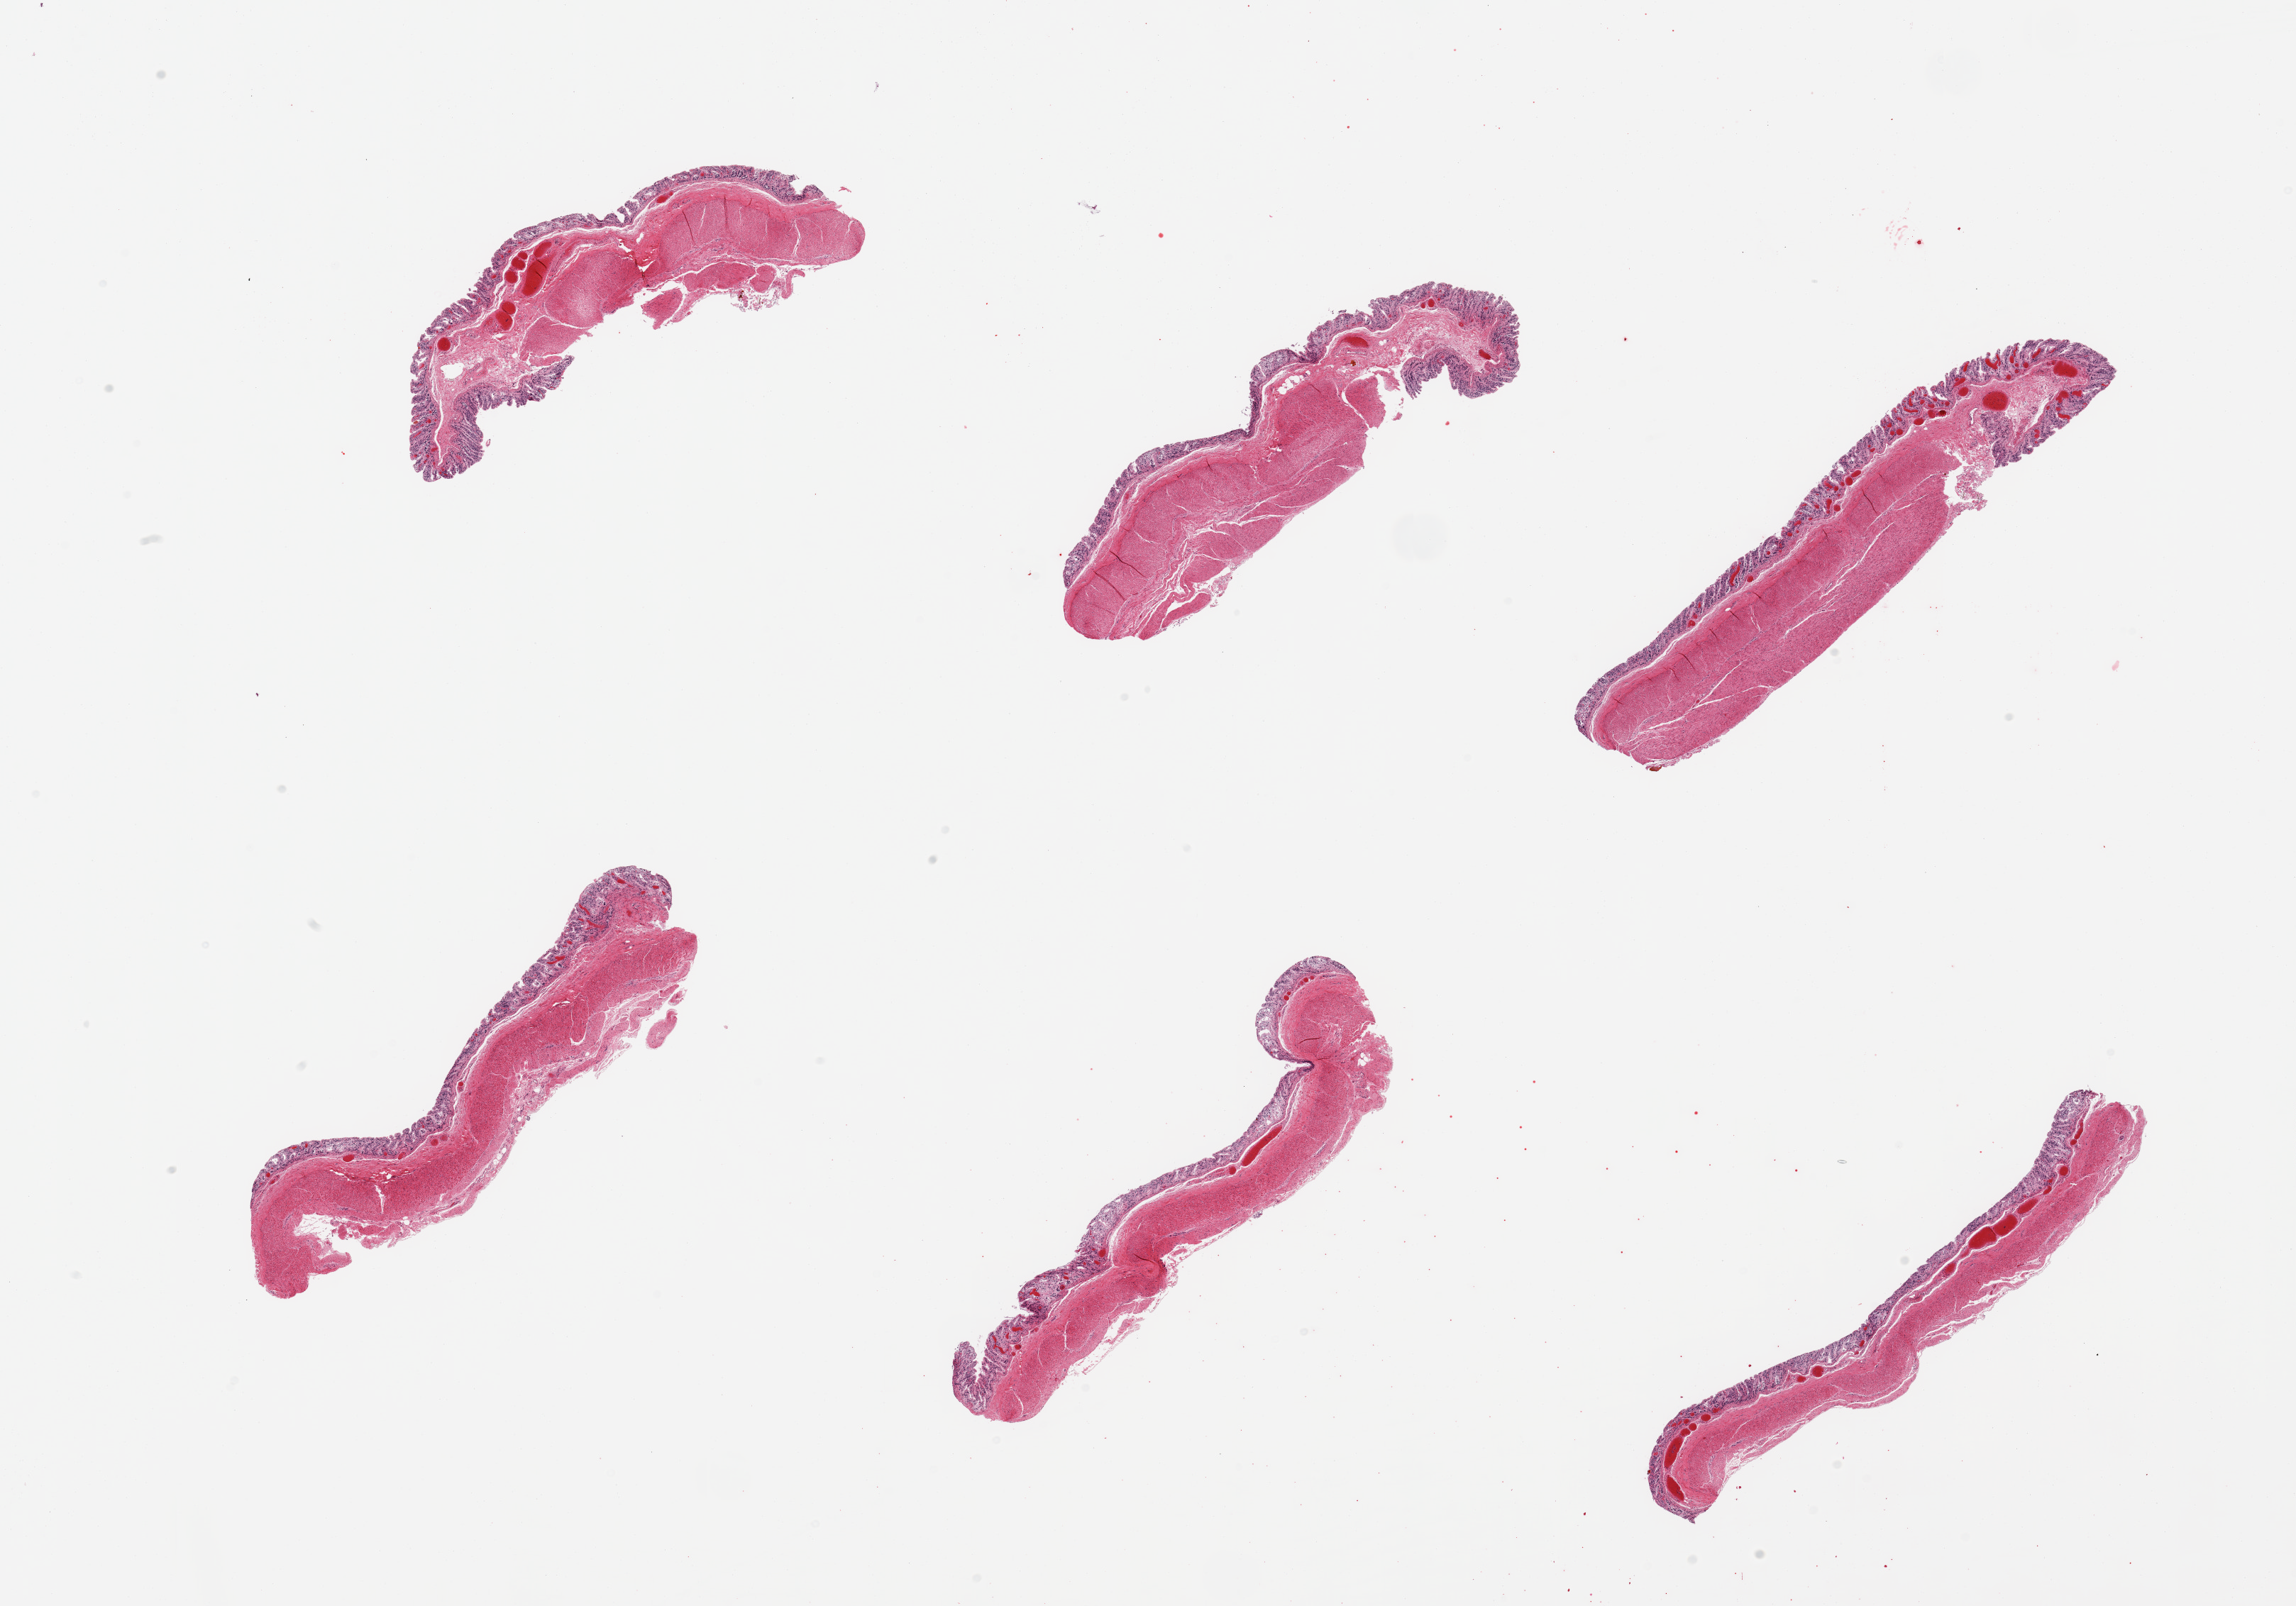
Haematoxylin and eosin whole-slide image, whole scanned area (about 25.6 x 17.9 mm) shown as a low-resolution overview. PAXgene-fixed, paraffin-embedded tissue. Sampled site (target tissue): transverse colon. Tissue donor sample. Male donor.
- pathologist's review note for this sample: 6 pieces; mucosal glands autolyzed, muscularis intact